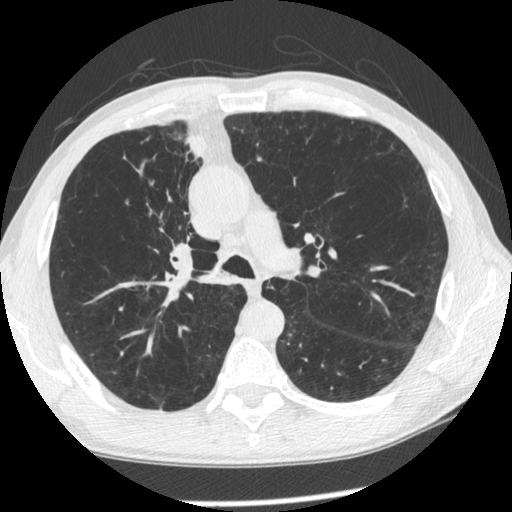
Low-dose screening chest CT, one axial slice. Position 155 of 261 along the scan axis. Reconstruction kernel STANDARD. 120 kVp. Lung window (W 1500 / L -600 HU). 512 × 512 image matrix, field of view 340 × 340 mm.
Structures marked on this image (outlined manually by an expert reader):
- lesion 1 (tumor, upper lobe of right lung): bounding box [x1, y1, x2, y2] px = [186, 134, 204, 157]